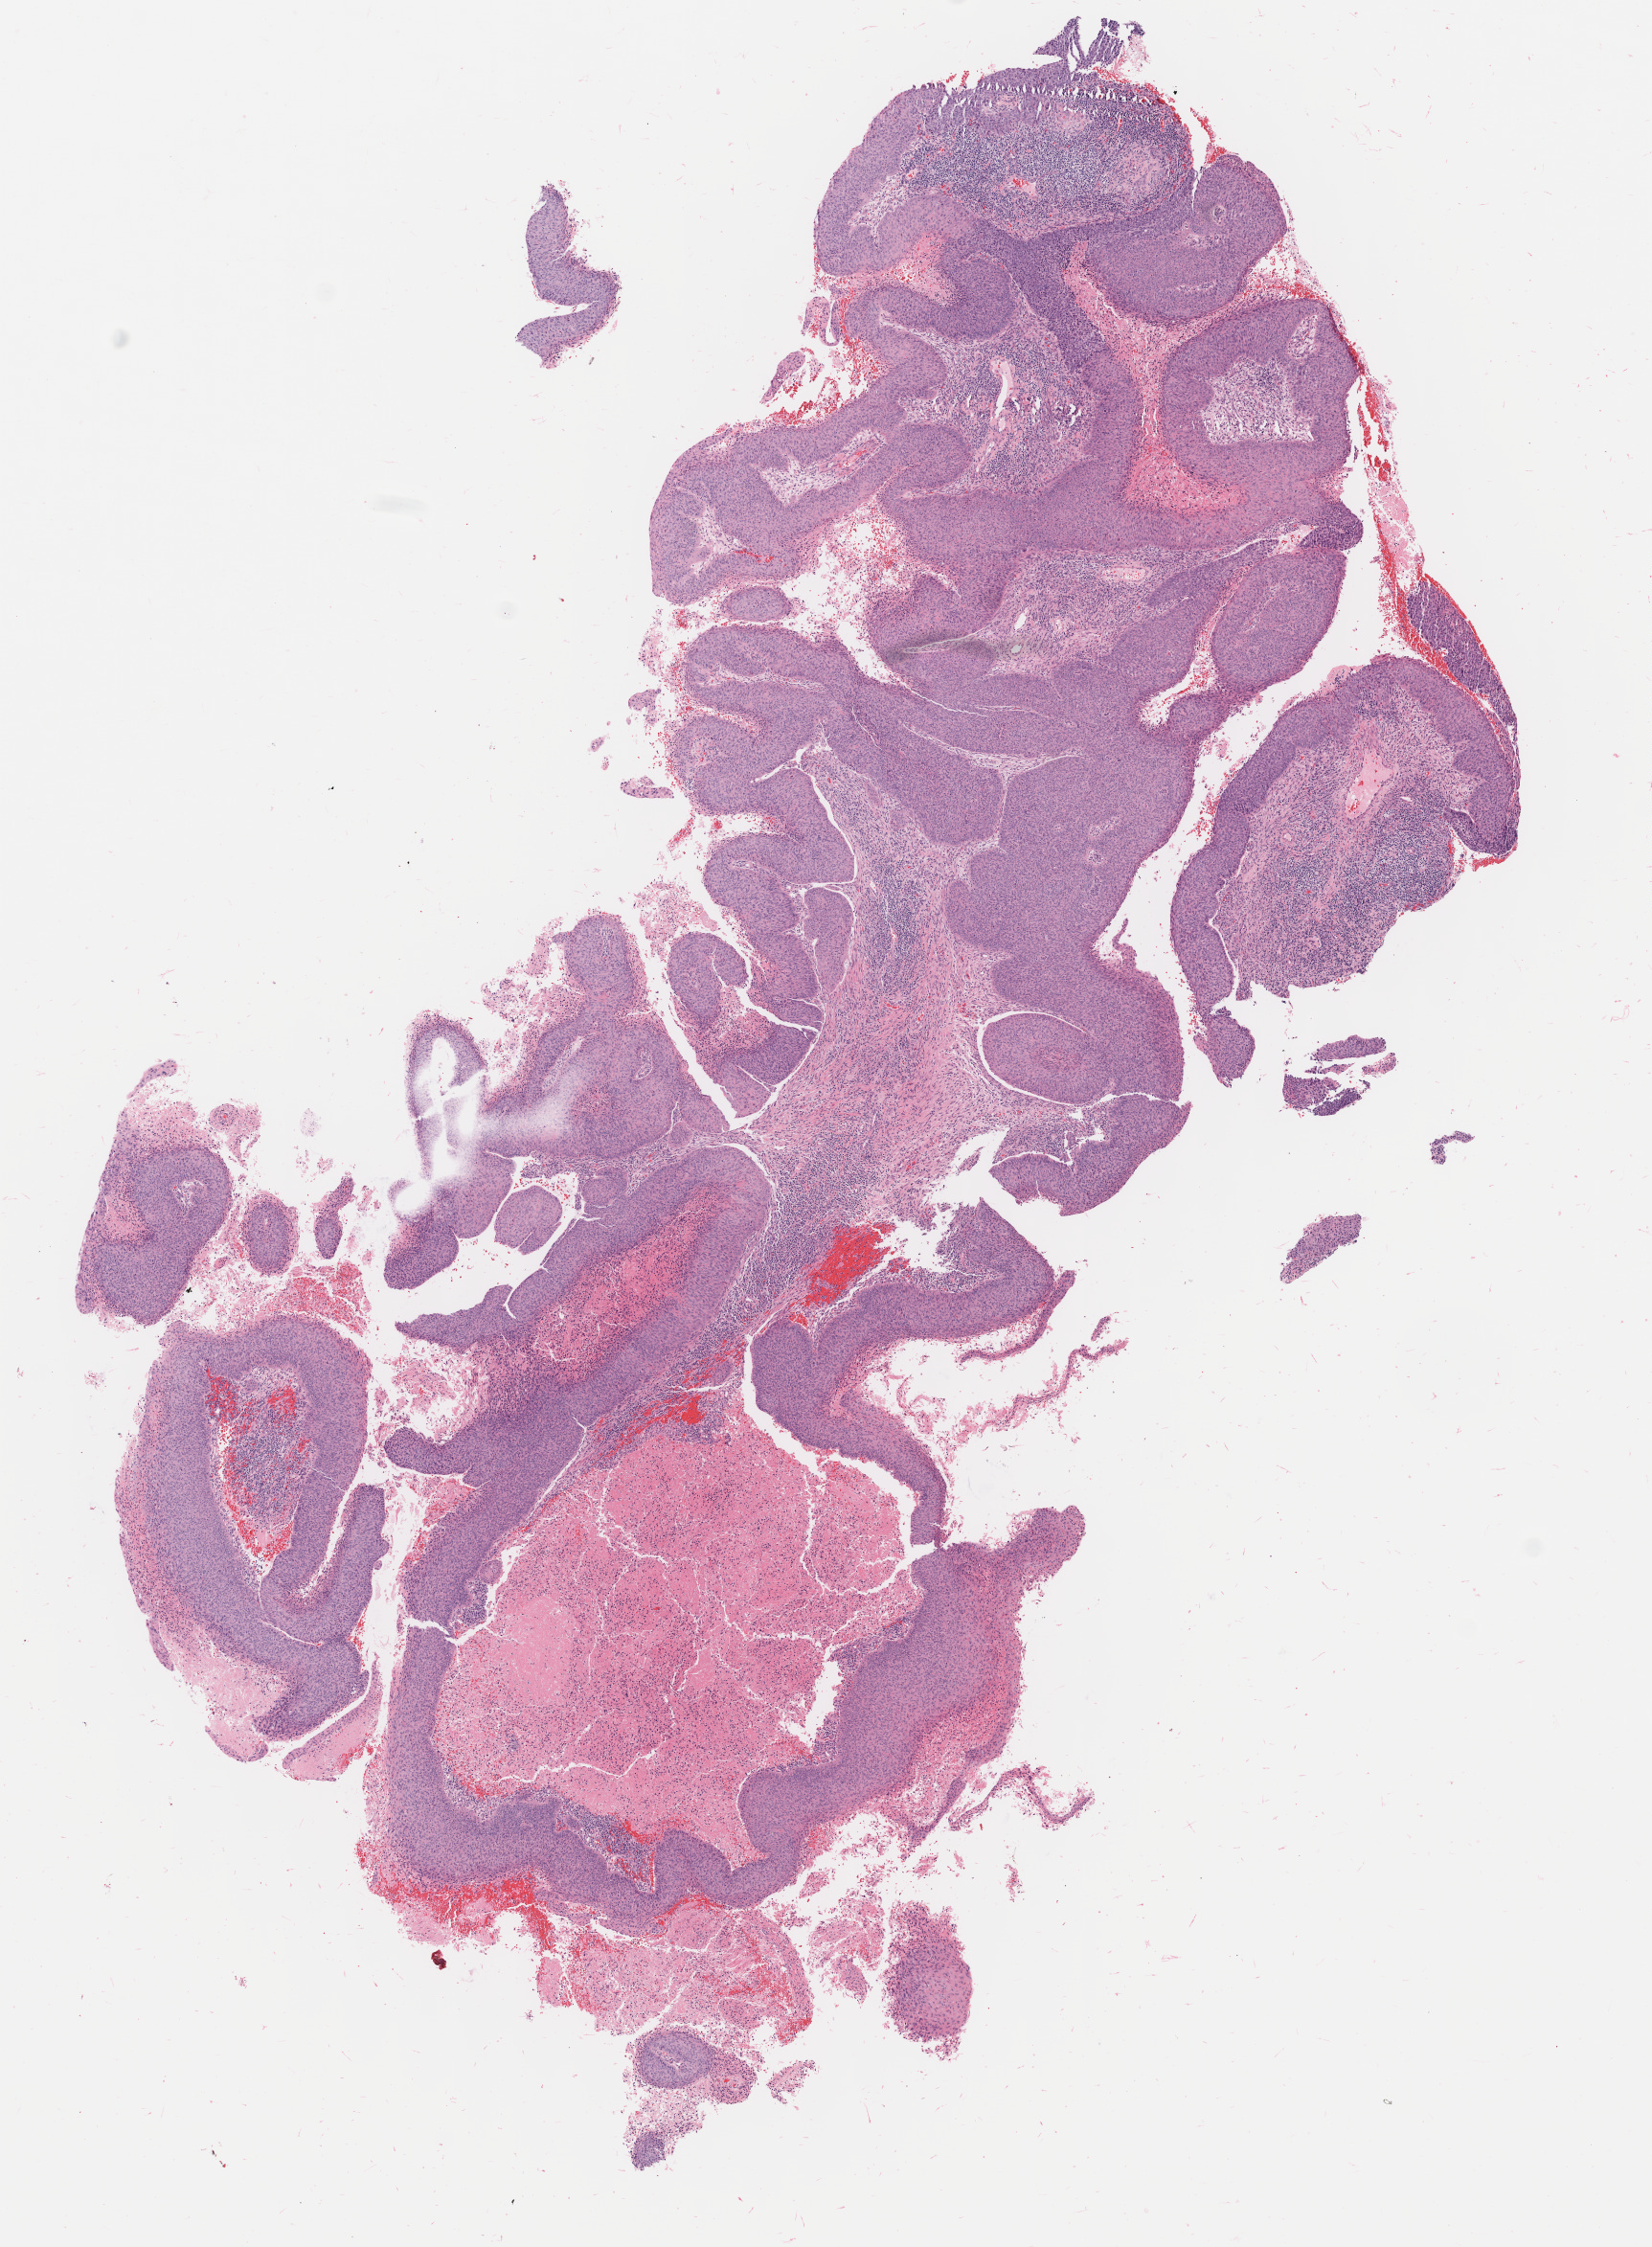
Digitized hematoxylin and eosin (H&E)-stained section, whole scanned area (about 6.9 x 9.3 mm) shown as a low-resolution overview, tumor tissue, site: cervix. Female patient, age 49 years.
Diagnosis: Squamous cell carcinoma, large cell, nonkeratinizing, NOS.